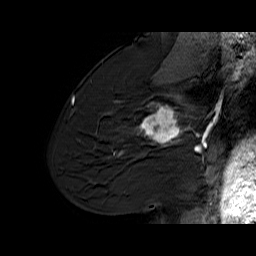
Breast MRI (dynamic contrast-enhanced), one sagittal slice. Slice 38 of 60 in the series (ordered by position). Dynamic contrast-enhanced series, time point 2 of 6 at this slice position (early post-contrast). 1.5 T. TE 6.1 ms, TR 32.9 ms. 4 mm slice thickness. 256 × 256 image matrix, field of view 220 × 220 mm. Female patient. From the clinical record (not read from this slice): setting: breast cancer imaged before/during neoadjuvant chemotherapy; receptor status: HER2-positive.
Structures marked on this image (semi-automatic segmentation, software-assisted and operator-edited):
- analysis volume of interest (the breast-tissue region the enhancement analysis was run in; not a lesion): bounding box (x1, y1, x2, y2) in pixels: (127, 95, 194, 165)
- tumour enhancement mask (voxels above the 100 % enhancement threshold inside the analysis volume of interest): (136, 95, 187, 146)